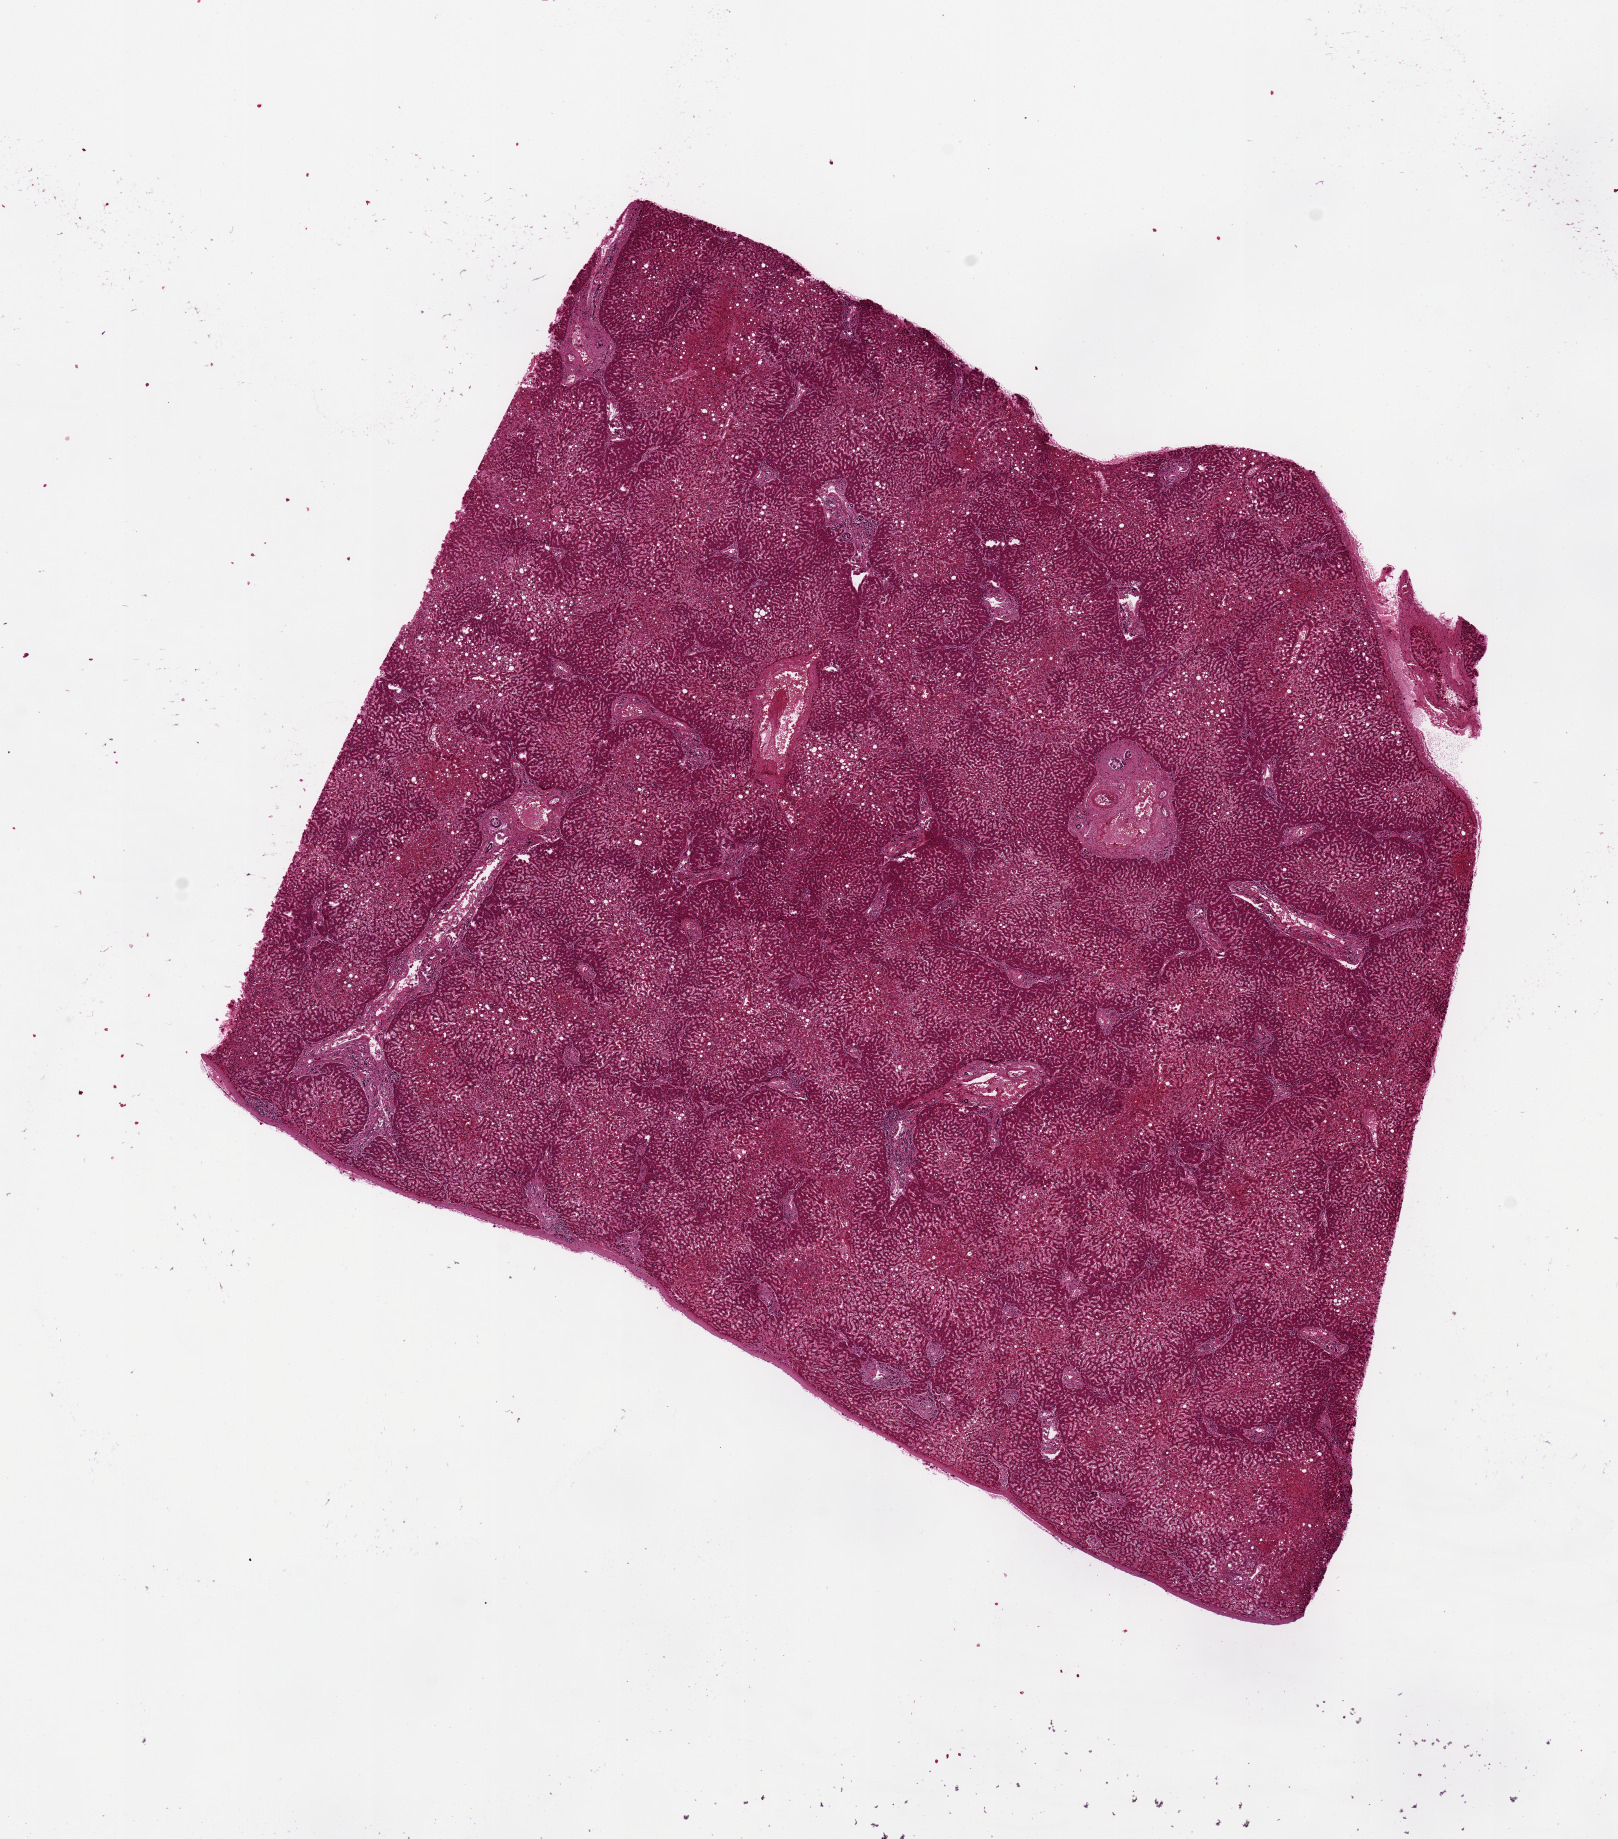
H&E whole-slide image, brightfield, whole scanned area (about 12.8 x 14.5 mm) shown as a low-resolution overview; PAXgene-fixed paraffin-embedded (PFPE) section; sampled site (target tissue): liver; tissue donor sample. Donor sex: male.
- pathologist's review note for this sample: Centrilobular ischemia and congestion 9x8.3mm. Capsule present in aliquot